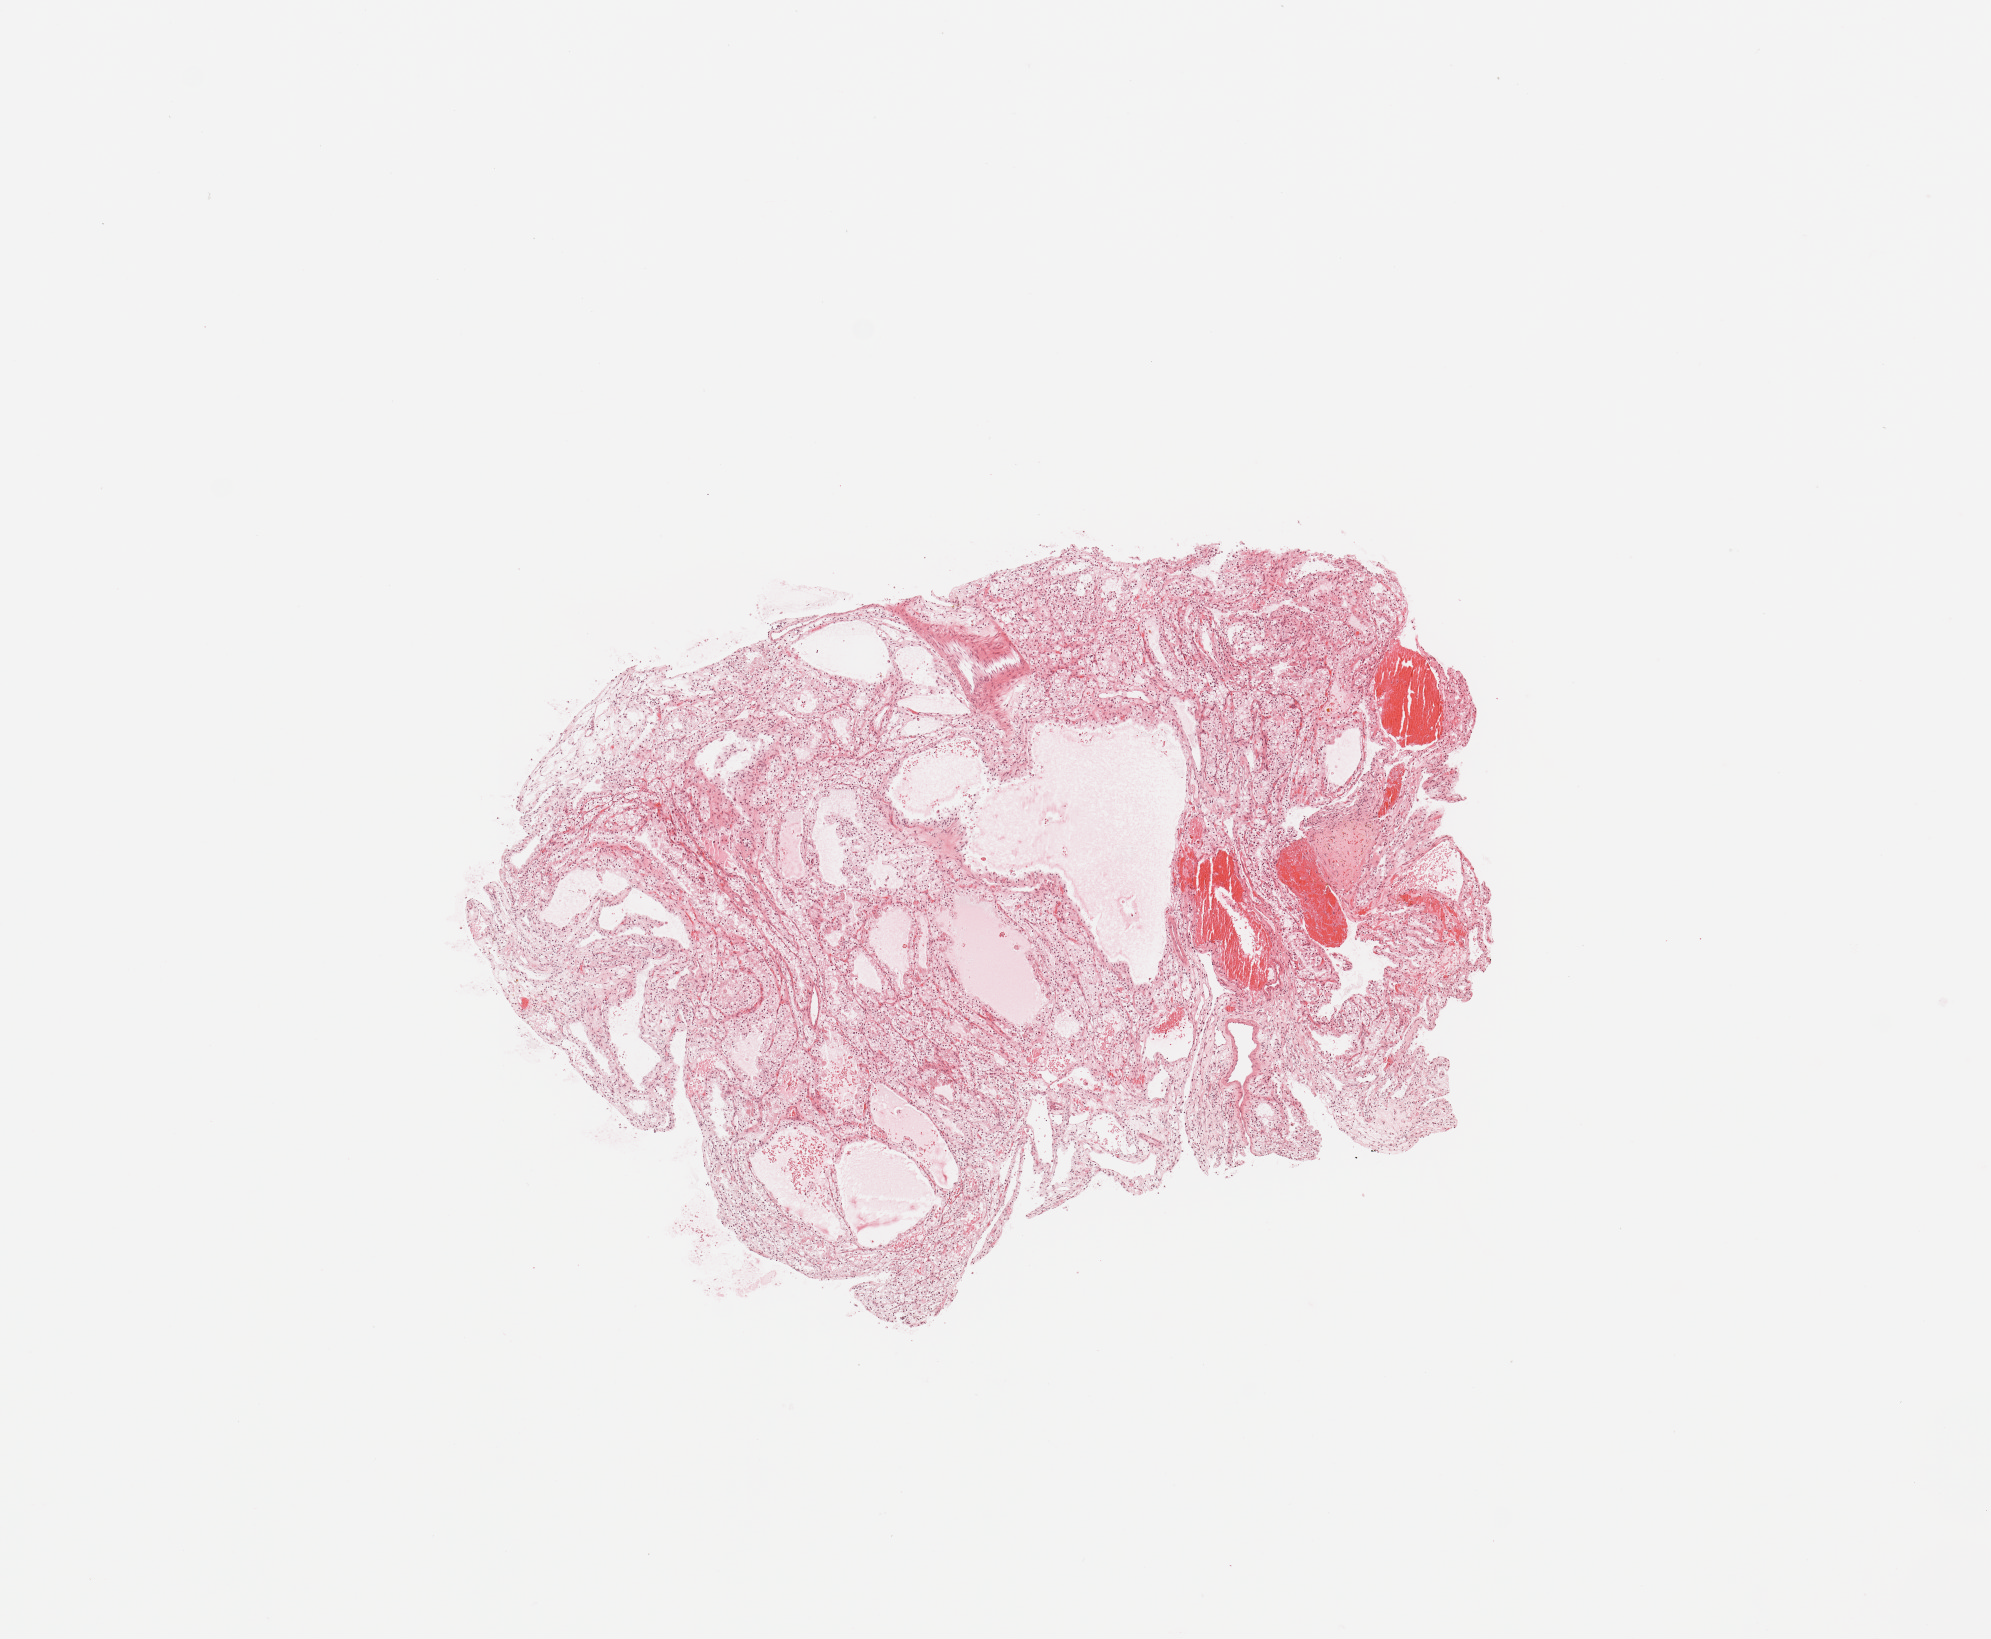
H&E whole-slide image — whole scanned area (about 7.9 x 6.5 mm, acquisition: 20x scan) shown as a low-resolution overview. Tumour tissue sample, sampled site: kidney. Patient: male, age 59 years. Histologic grade: G2 (moderately differentiated). Pathologist review of this section (percent, as recorded): tumour nuclei 85%, necrosis 0%.
• AJCC pathologic stage: I
• primary tumour site (as recorded): lower pole
• diagnosis: Renal cell carcinoma, NOS